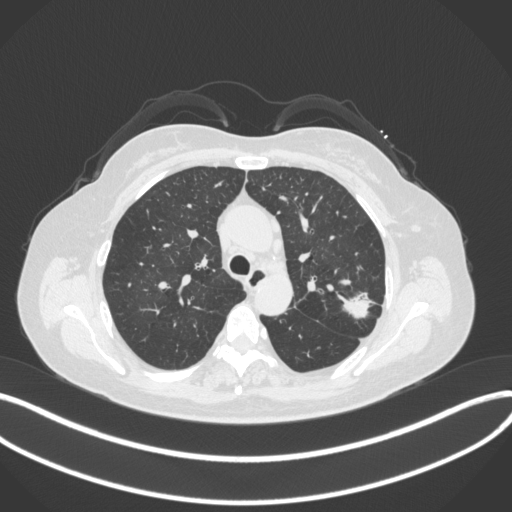
Chest CT, one axial slice. 120 kVp. Lung window (W 1500 / L -600 HU). 1 mm slice thickness. 512 × 512 image matrix, field of view 400 × 400 mm. Patient: female, 60 years. From the clinical record (not read from this slice): clinical TNM (as recorded): T1c N0 M0.
Structures marked on this image (rectangle marked by the reading radiologist):
- lung tumour (recorded histology: adenocarcinoma): box from (x=337, y=286) to (x=376, y=328) px